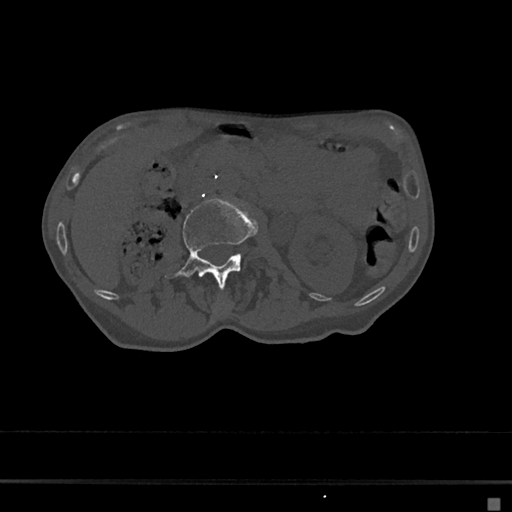
CT including the spine, one axial slice. Slice 12 of 797 in the series (ordered by position). Reconstruction kernel Br40s/3. 120 kVp. Bone window (W 1800 / L 400 HU). 0.5 mm slice thickness. 512 × 512 image matrix, field of view 360 × 360 mm. Patient: female, 68 years. From the clinical record (not read from this slice): primary cancer: renal.
Annotated regions visible in this slice (semi-automatic segmentation, software-assisted and operator-edited):
- L1 vertebra: bounding box <223,300,226,306> (left, top, right, bottom; pixels)
- L2 vertebra: <164,198,258,287>